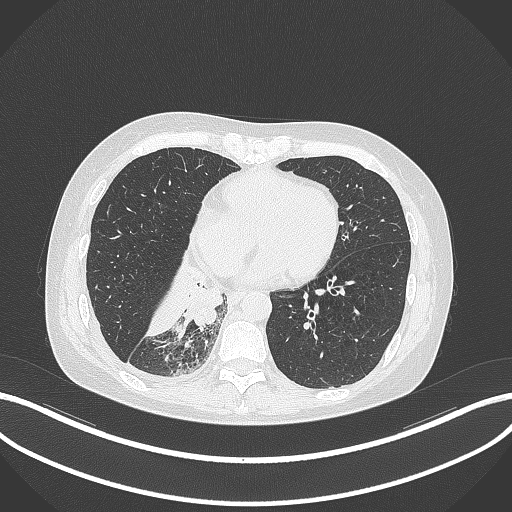
Chest CT, one axial slice; slice 108 of 329 in the series (ordered by position); lung window (W 1500 / L -600 HU); 1 mm slice thickness; 512 × 512 image matrix, field of view 400 × 400 mm. Patient: female, 63 years. From the clinical record (not read from this slice): clinical TNM (as recorded): T1c N0 M0.
Structures marked on this image (bounding box drawn by a radiologist):
- lung tumour (recorded histology: adenocarcinoma): box from (x=180, y=275) to (x=224, y=329) px